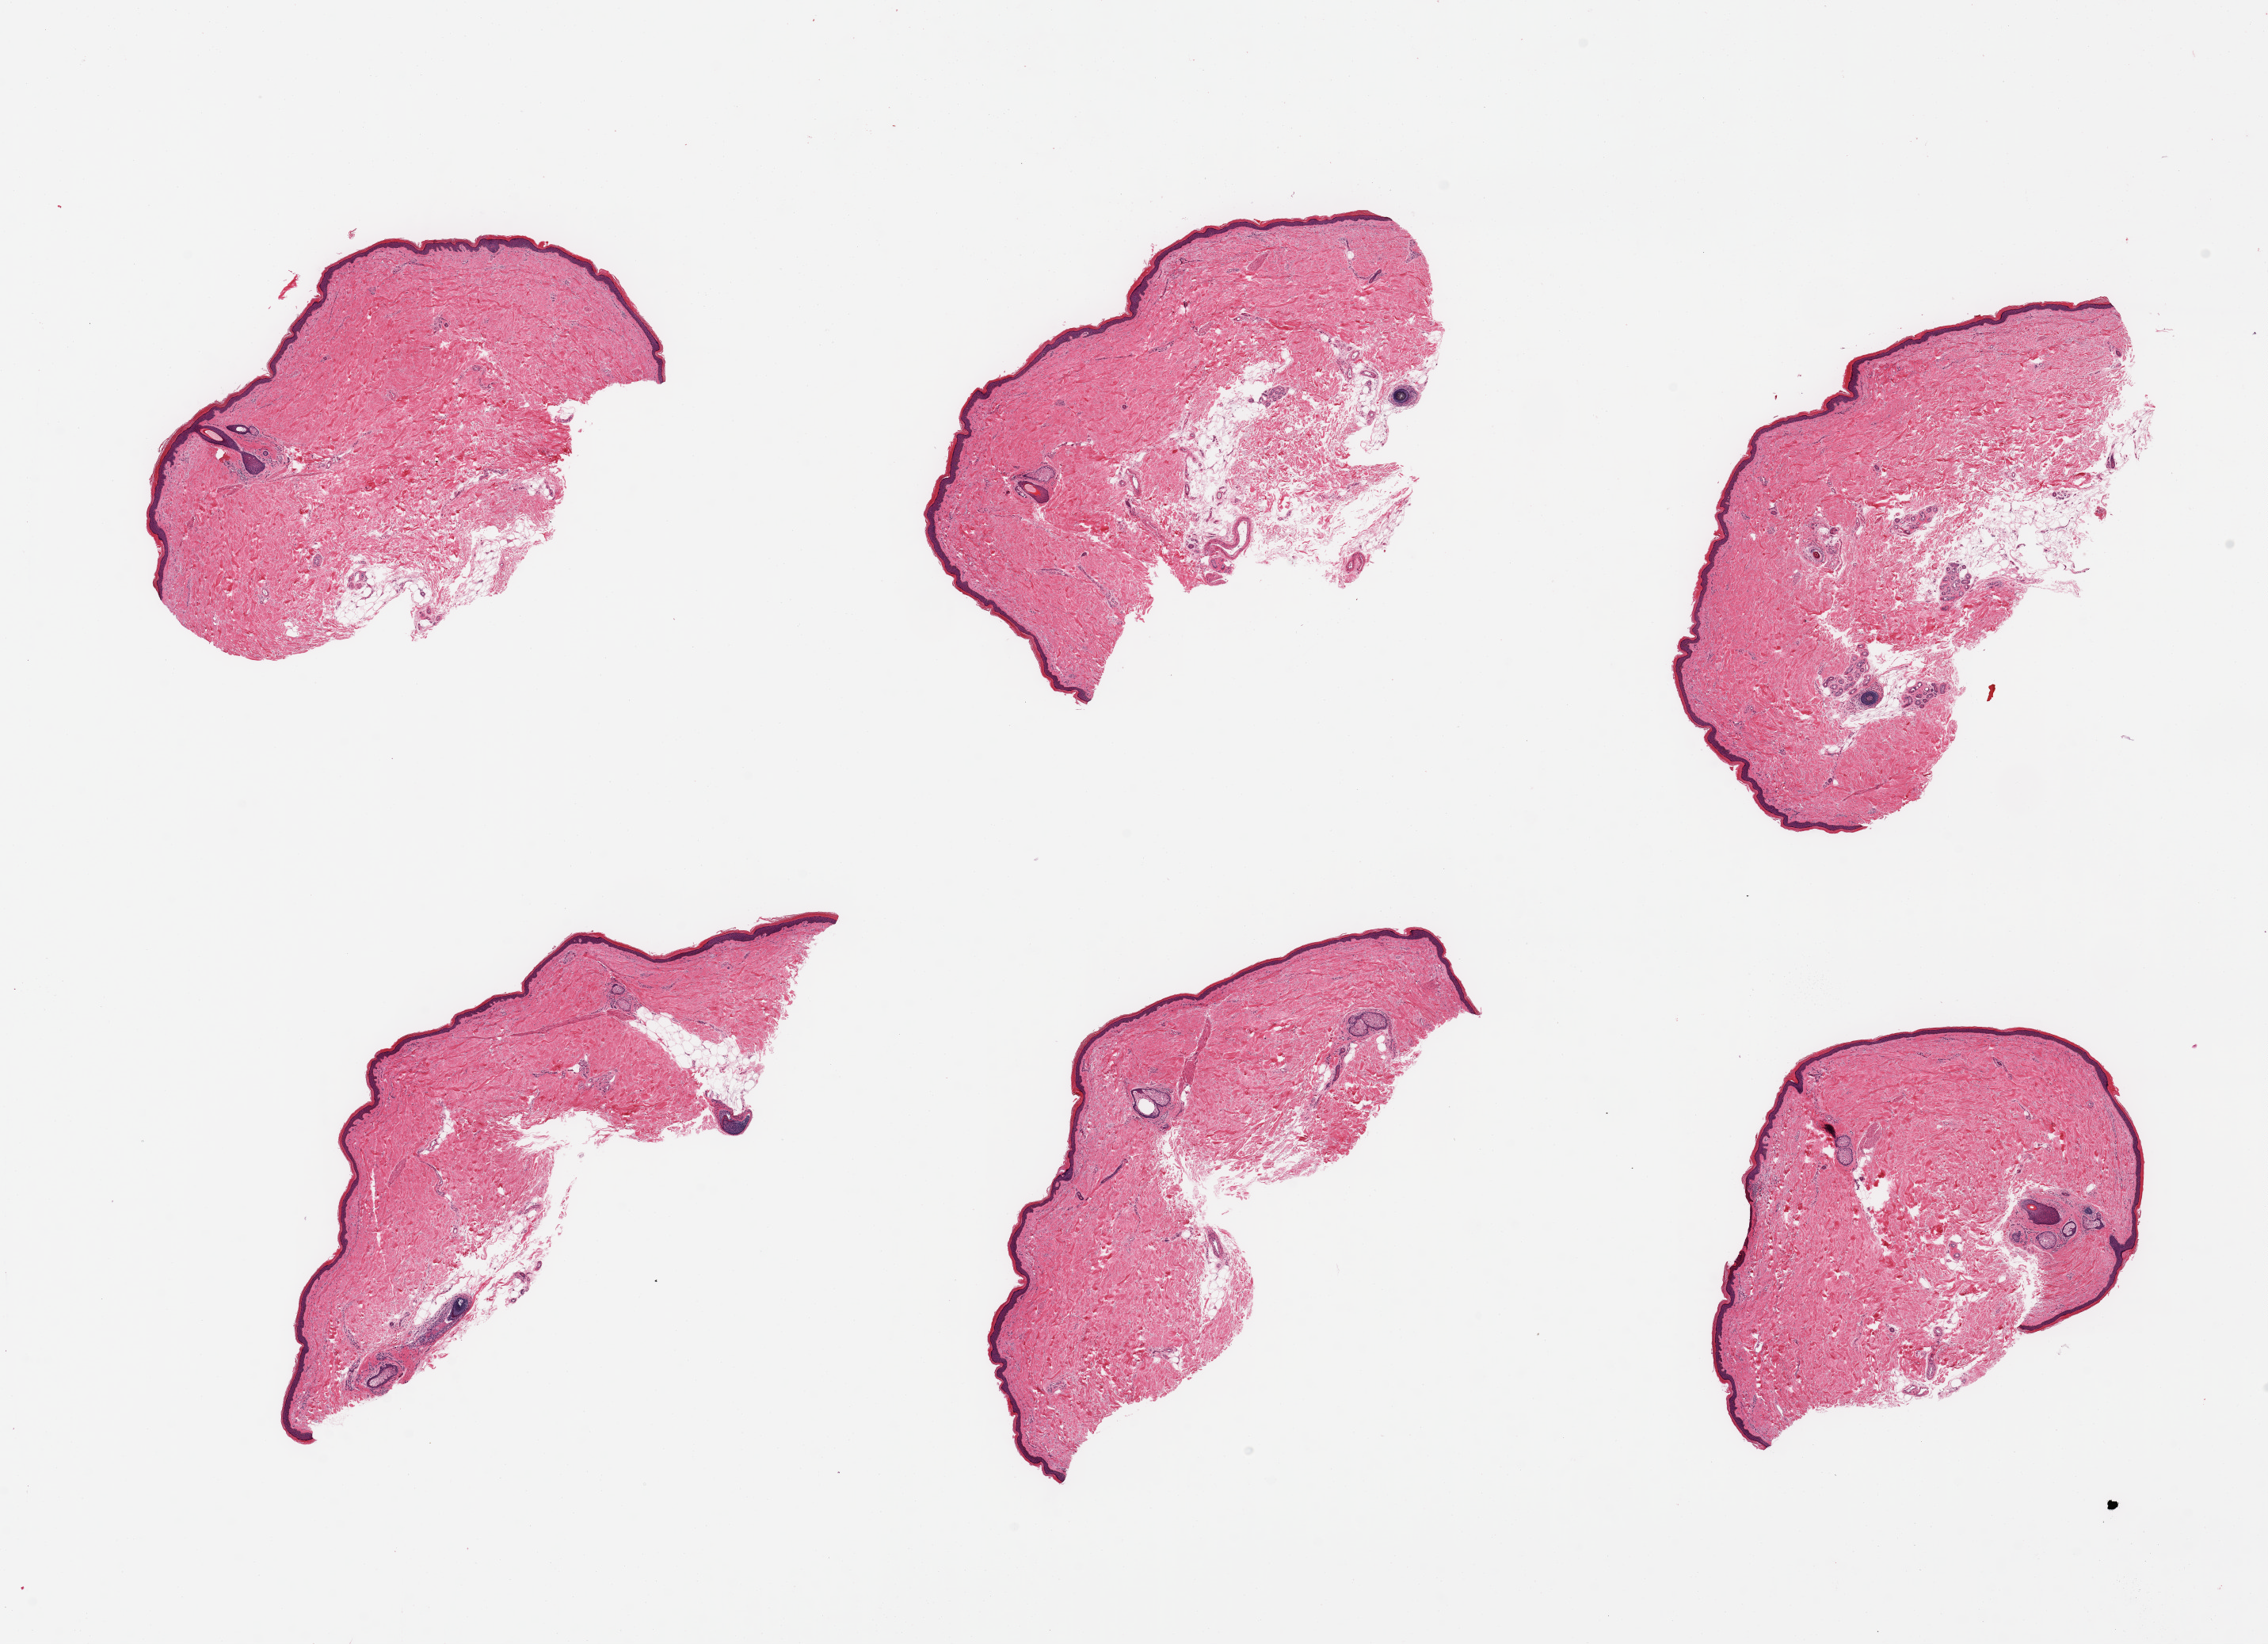
Hematoxylin and eosin (H&E) whole-slide image — shown as a low-resolution overview of the whole scanned area (about 22.6 x 16.4 mm, slide scanned at 20x), PAXgene-fixed paraffin-embedded (PFPE) section, target tissue: skin of lower leg, donor tissue sample. Donor sex: male.
• pathologist's review note for this sample: 6 pieces, trace adherent dermal fat; squamous epithelium is ~35-40 microns